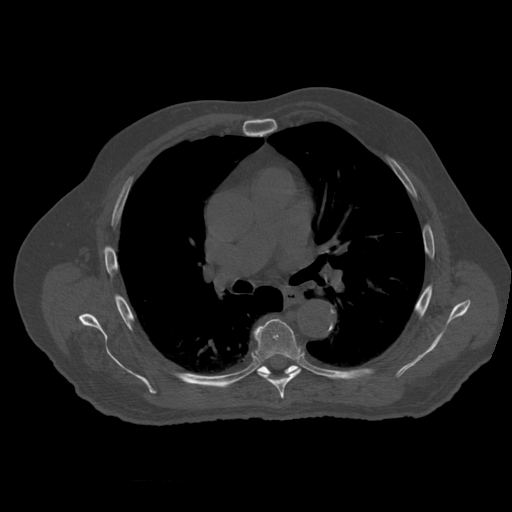
CT including the spine, one axial slice. Position 375 of 399 along the scan axis. 120 kVp. Bone window (W 1800 / L 400 HU). 1.25 mm slice thickness. 512 × 512 image matrix. Patient age 73 years. From the clinical record (not read from this slice): primary cancer: prostate.
Annotated regions visible in this slice (semi-automatically segmented with operator editing):
- T6 vertebra: box from (x=253, y=319) to (x=302, y=399) px
- T7 vertebra: (x=258, y=365)–(x=300, y=375)